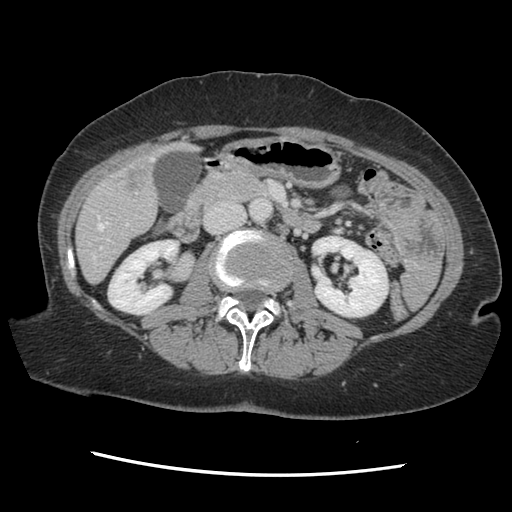
Contrast-enhanced abdominal CT, one axial slice. Position 54 of 141 along the scan axis. 120 kVp. Soft-tissue window (W 400 / L 40 HU). 2.5 mm slice thickness. 512 × 512 image matrix, field of view 330 × 330 mm. Female patient, age 61 years. From the clinical record (not read from this slice): diagnosis: colorectal cancer liver metastases, imaged before liver resection; multiple liver metastases: no; largest metastasis: 2.4 cm.
Outlined on this slice (expert manual segmentation):
- hepatic veins: bounding box (x1, y1, x2, y2) in pixels: (93, 157, 154, 263)
- liver: (77, 143, 193, 282)
- planned liver remnant (the part of the liver to remain after resection): (77, 193, 158, 282)
- portal vein (with intrahepatic branches): (100, 223, 129, 249)
- liver metastasis: (123, 160, 153, 197)